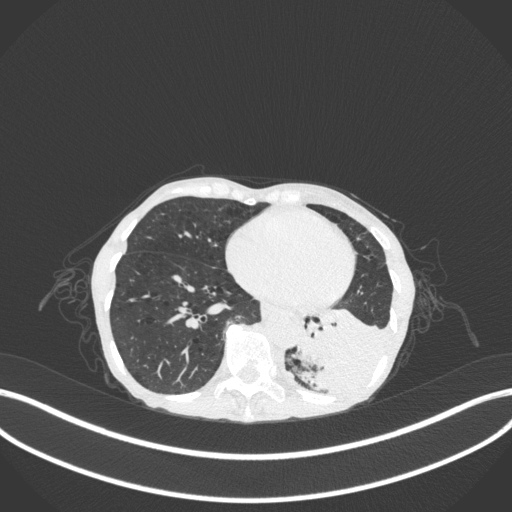
Chest CT, one axial slice. Slice 80 of 347 in the series (ordered by position). 120 kVp. Lung window (W 1500 / L -600 HU). 1 mm slice thickness. 512 × 512 image matrix. Patient: female, 70 years. Case-level facts recorded for this patient, not image findings: clinical TNM (as recorded): T3 N0 M0.
Outlined on this slice (rectangle marked by the reading radiologist):
- lung tumour (recorded histology: small cell carcinoma): bounding box [x1, y1, x2, y2] px = [294, 296, 393, 401]